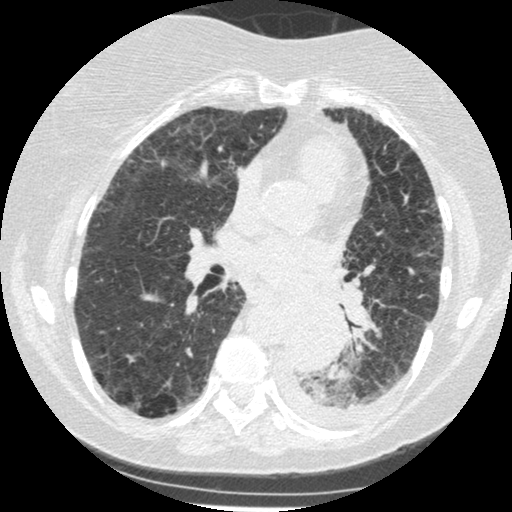
Low-dose screening chest CT, one axial slice; position 123 of 341 along the scan axis; reconstruction kernel STANDARD; 120 kVp; lung window (W 1500 / L -600 HU); 1.25 mm slice thickness; 512 × 512 image matrix.
Structures marked on this image (manually delineated by an expert):
- lesion 1 (tumor, lower lobe of left lung): bounding box [x1, y1, x2, y2] px = [284, 302, 345, 374]